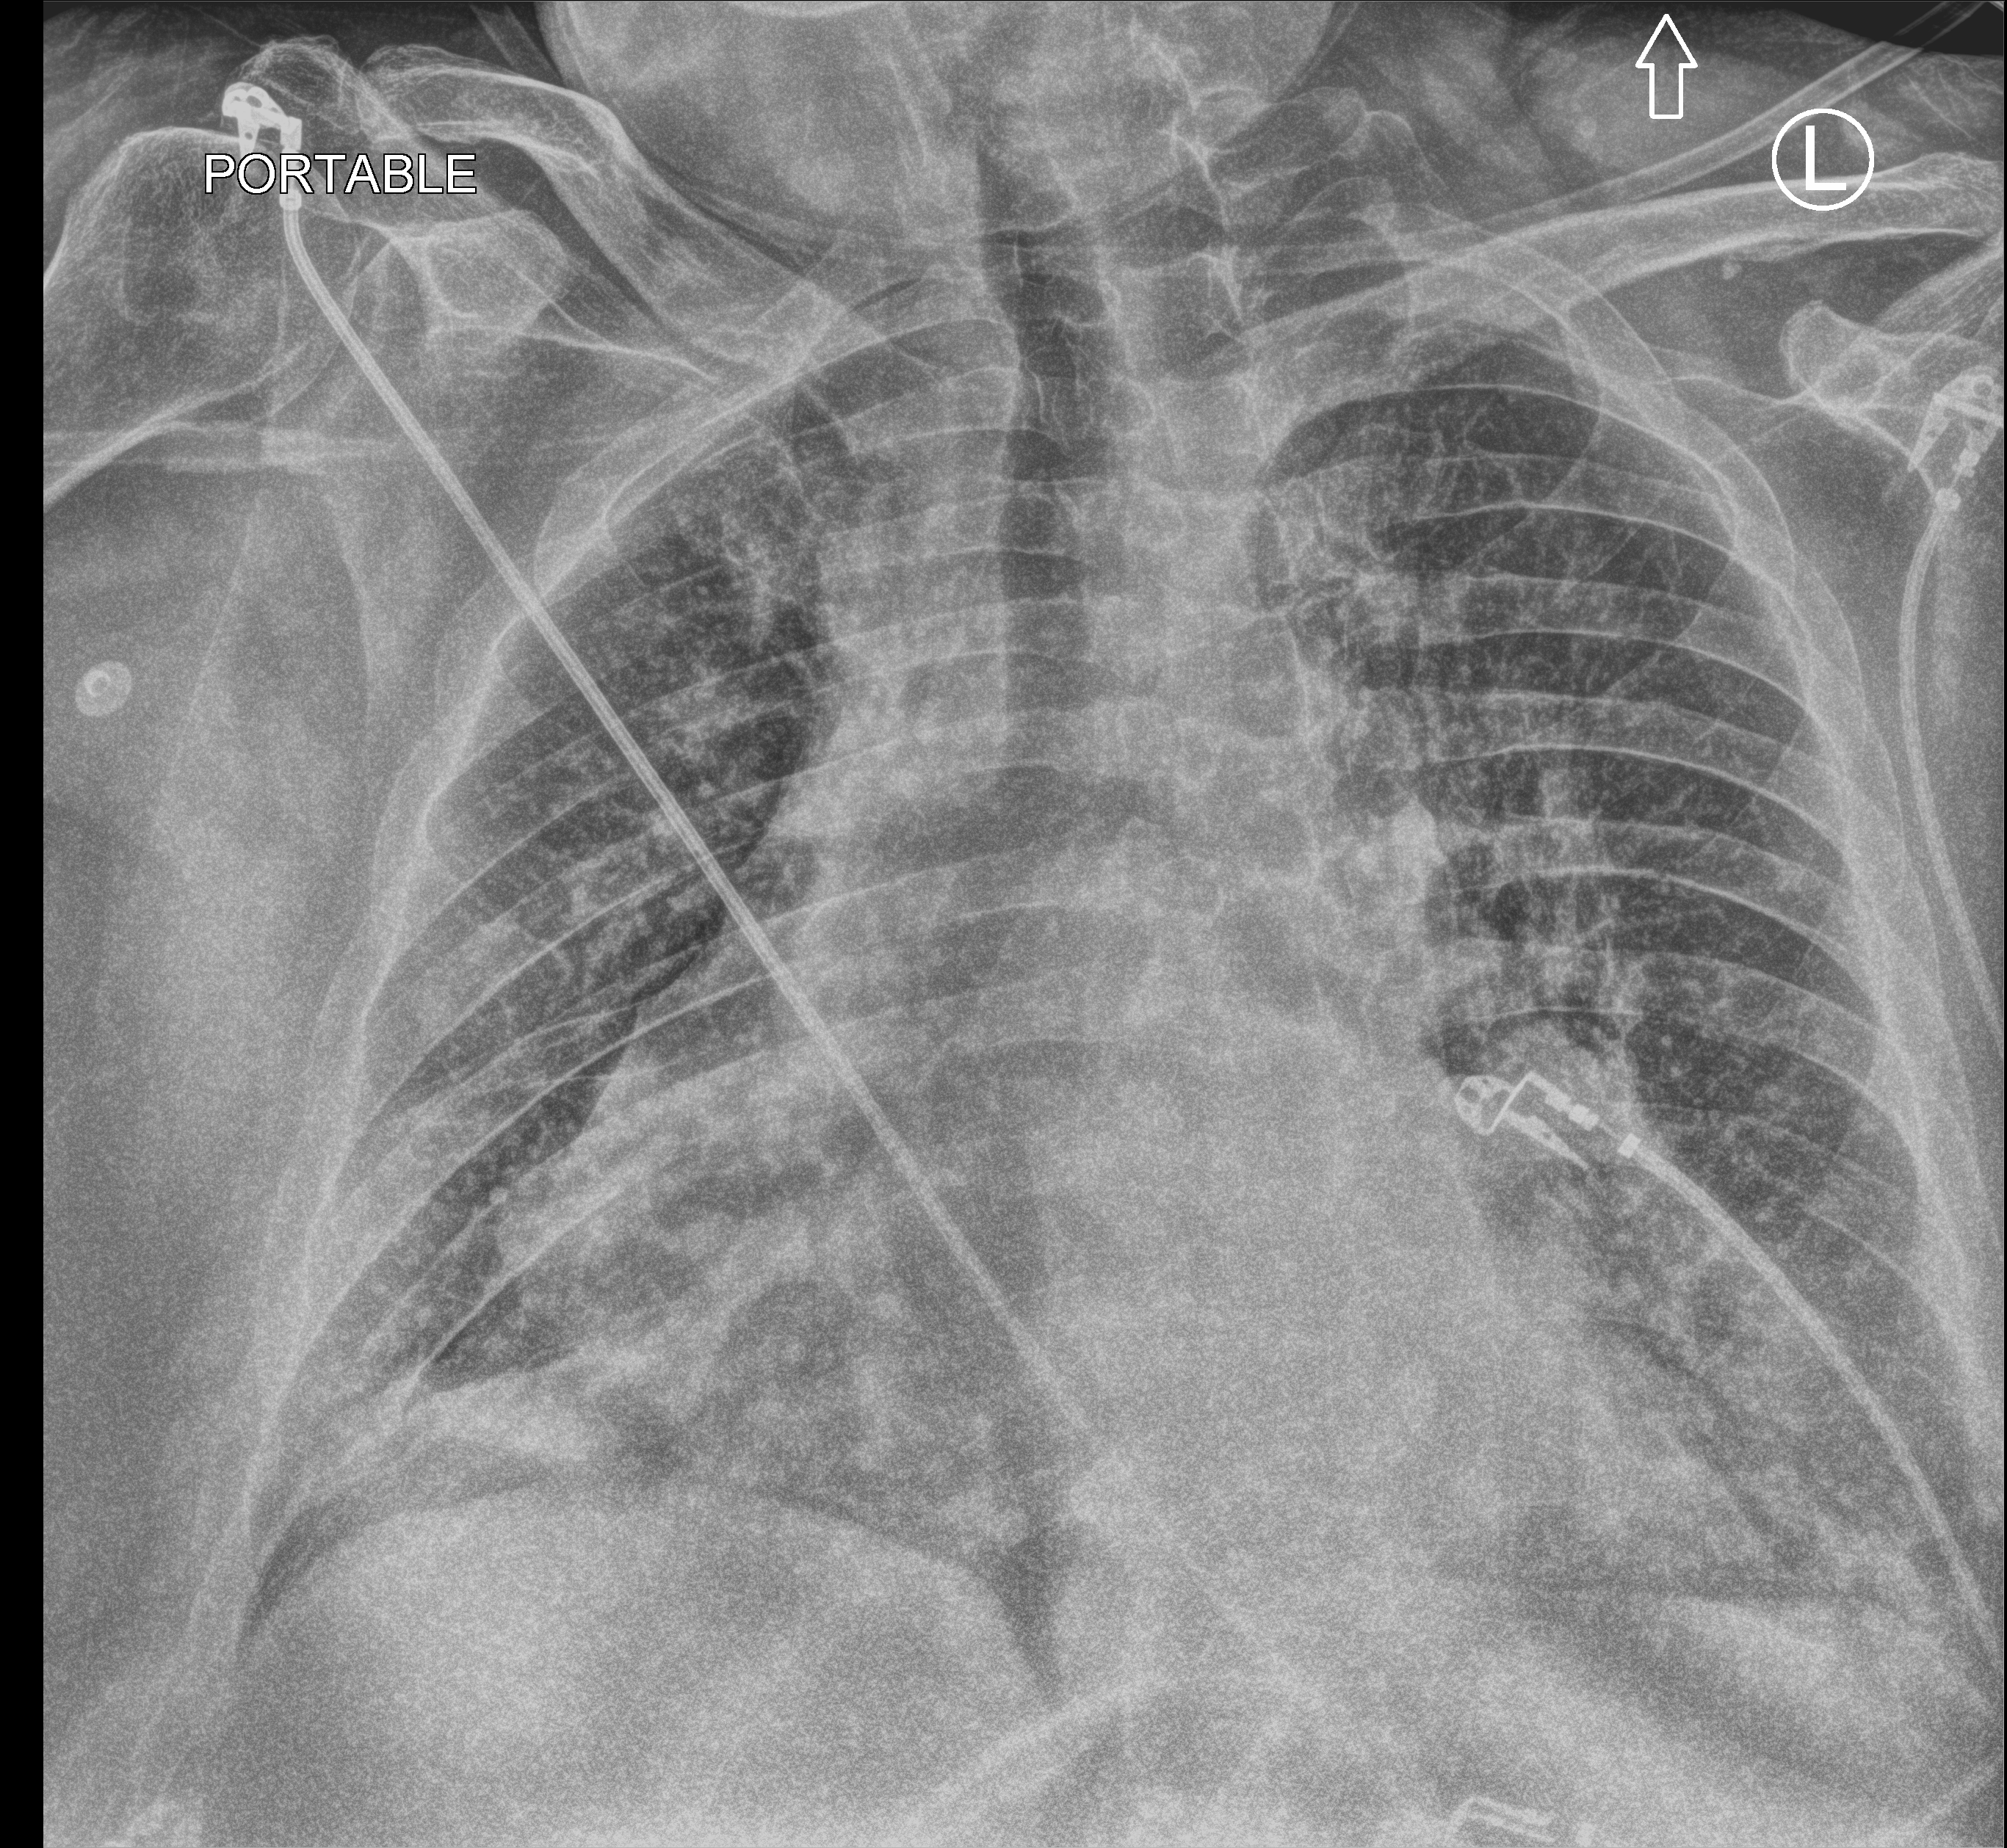
Bedside chest radiograph (computed radiography); anteroposterior (AP) projection. Male patient hospitalised with COVID-19, age 60–74 years.
Admission-level facts for this patient (not findings on this image; timing relative to this image not recorded): mechanically ventilated during this hospital stay: yes; length of hospital stay: 10 days; admitted to intensive care during this hospital stay: yes.